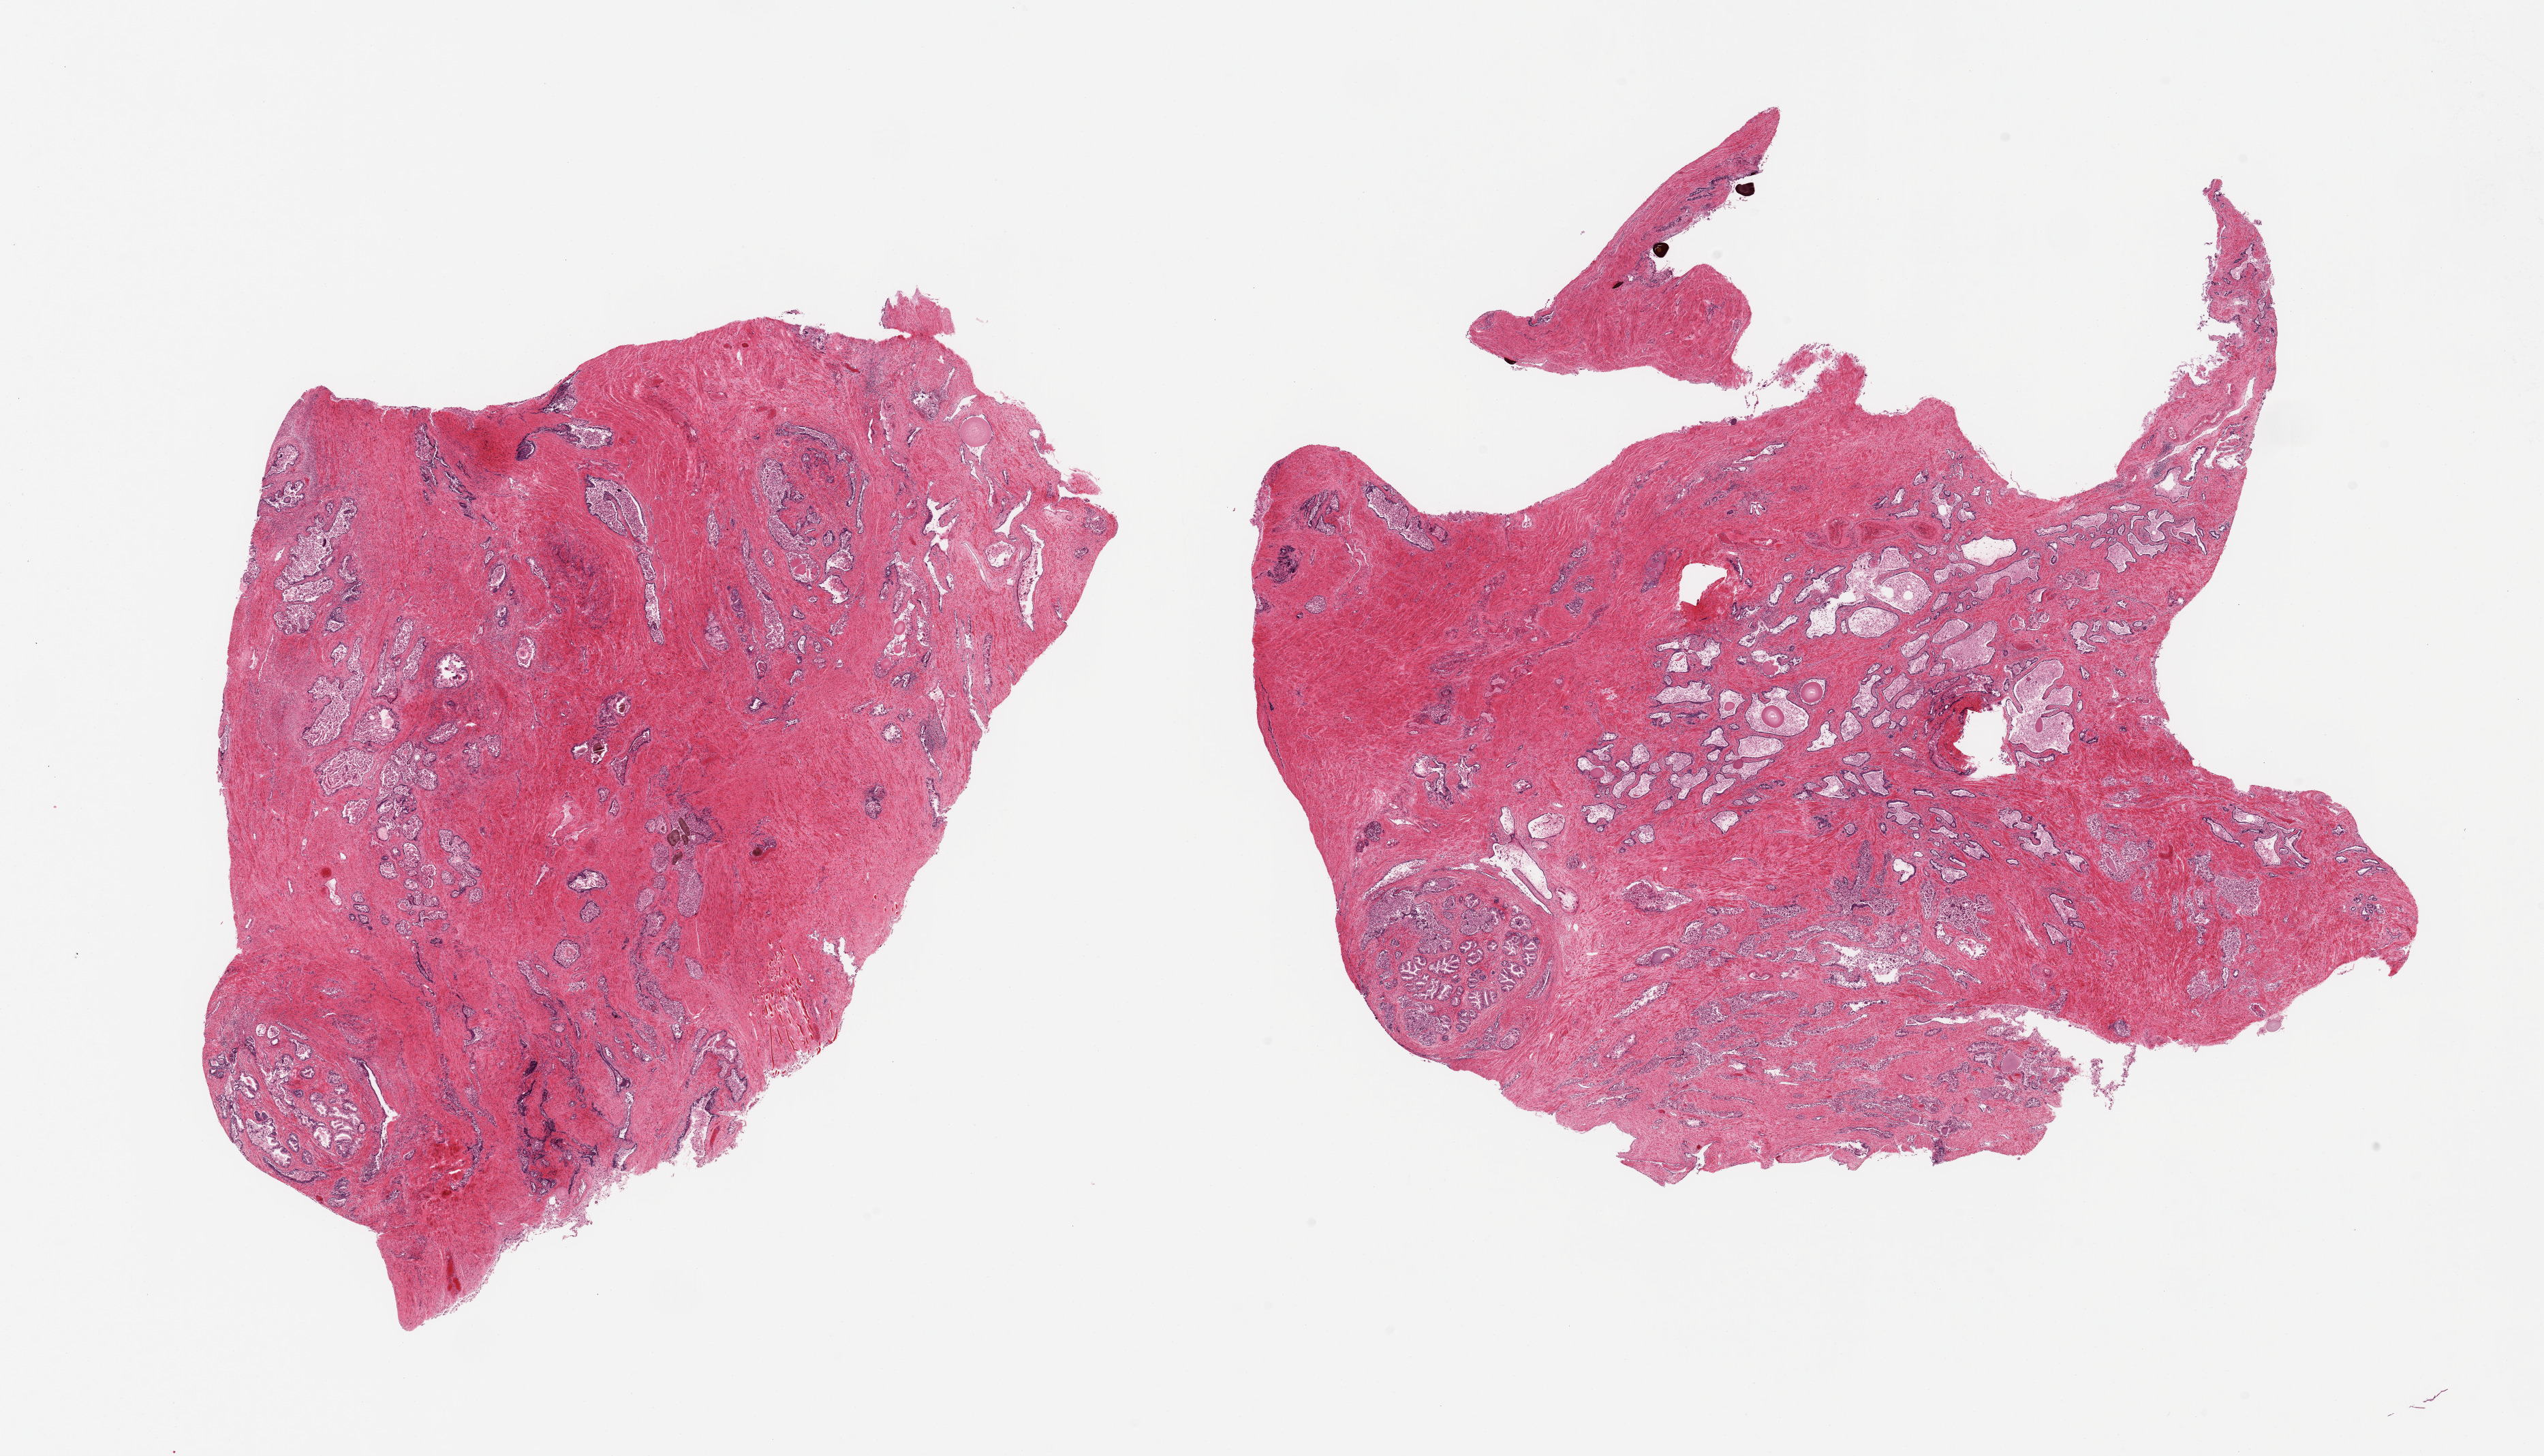
Whole-slide image, hematoxylin and eosin (H&E) stain, brightfield, whole scanned area (about 29.5 x 16.9 mm) shown as a low-resolution overview; PAXgene-fixed, paraffin-embedded tissue; sampled site (target tissue): prostate; tissue donor sample. Donor sex: male.
Review note (as recorded): 2 pieces, glandular elements with moderate-advanced autolysis/lsloughing mucosa.